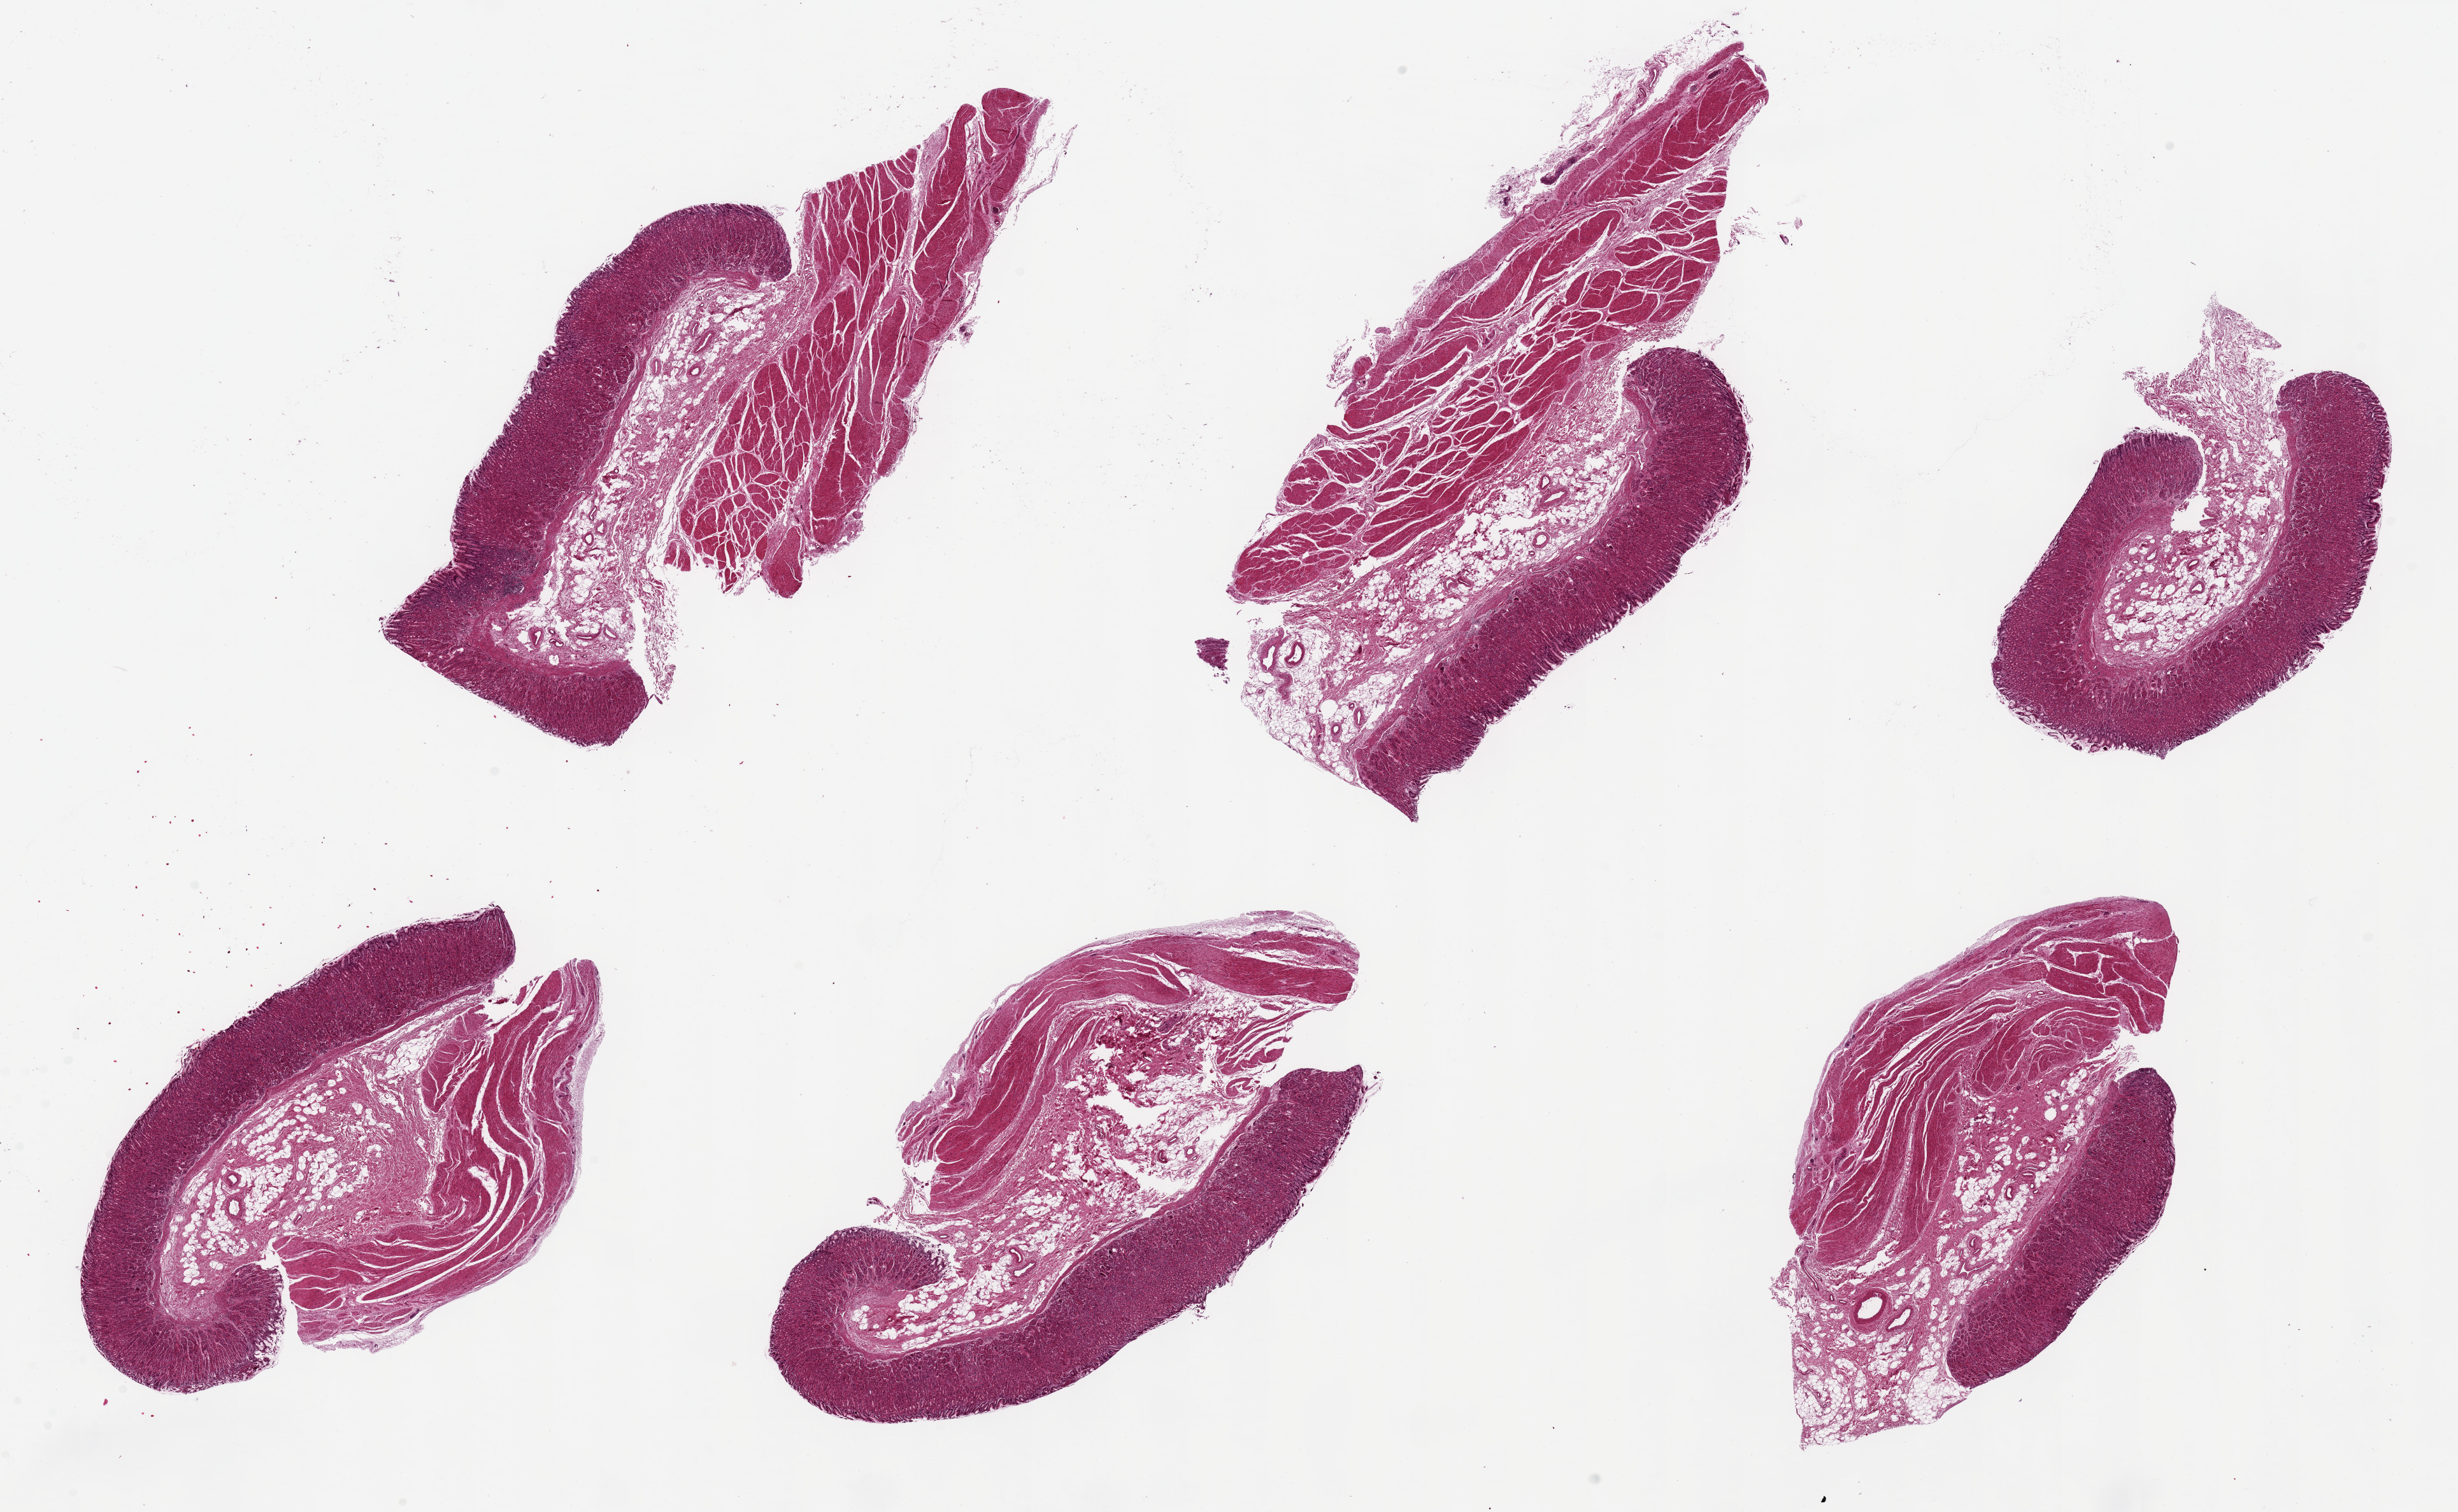
Haematoxylin and eosin whole-slide image, brightfield — low-resolution overview of the scanned area, about 30.5 x 18.8 mm (acquisition: 20x scan). PAXgene-fixed paraffin-embedded (PFPE) section. Sampled site (target tissue): stomach. Tissue donor sample.
• review note (as recorded): 6 pieces, up to 11x5mm; mucosa is well preserved, ~25% of thickness, rep layer